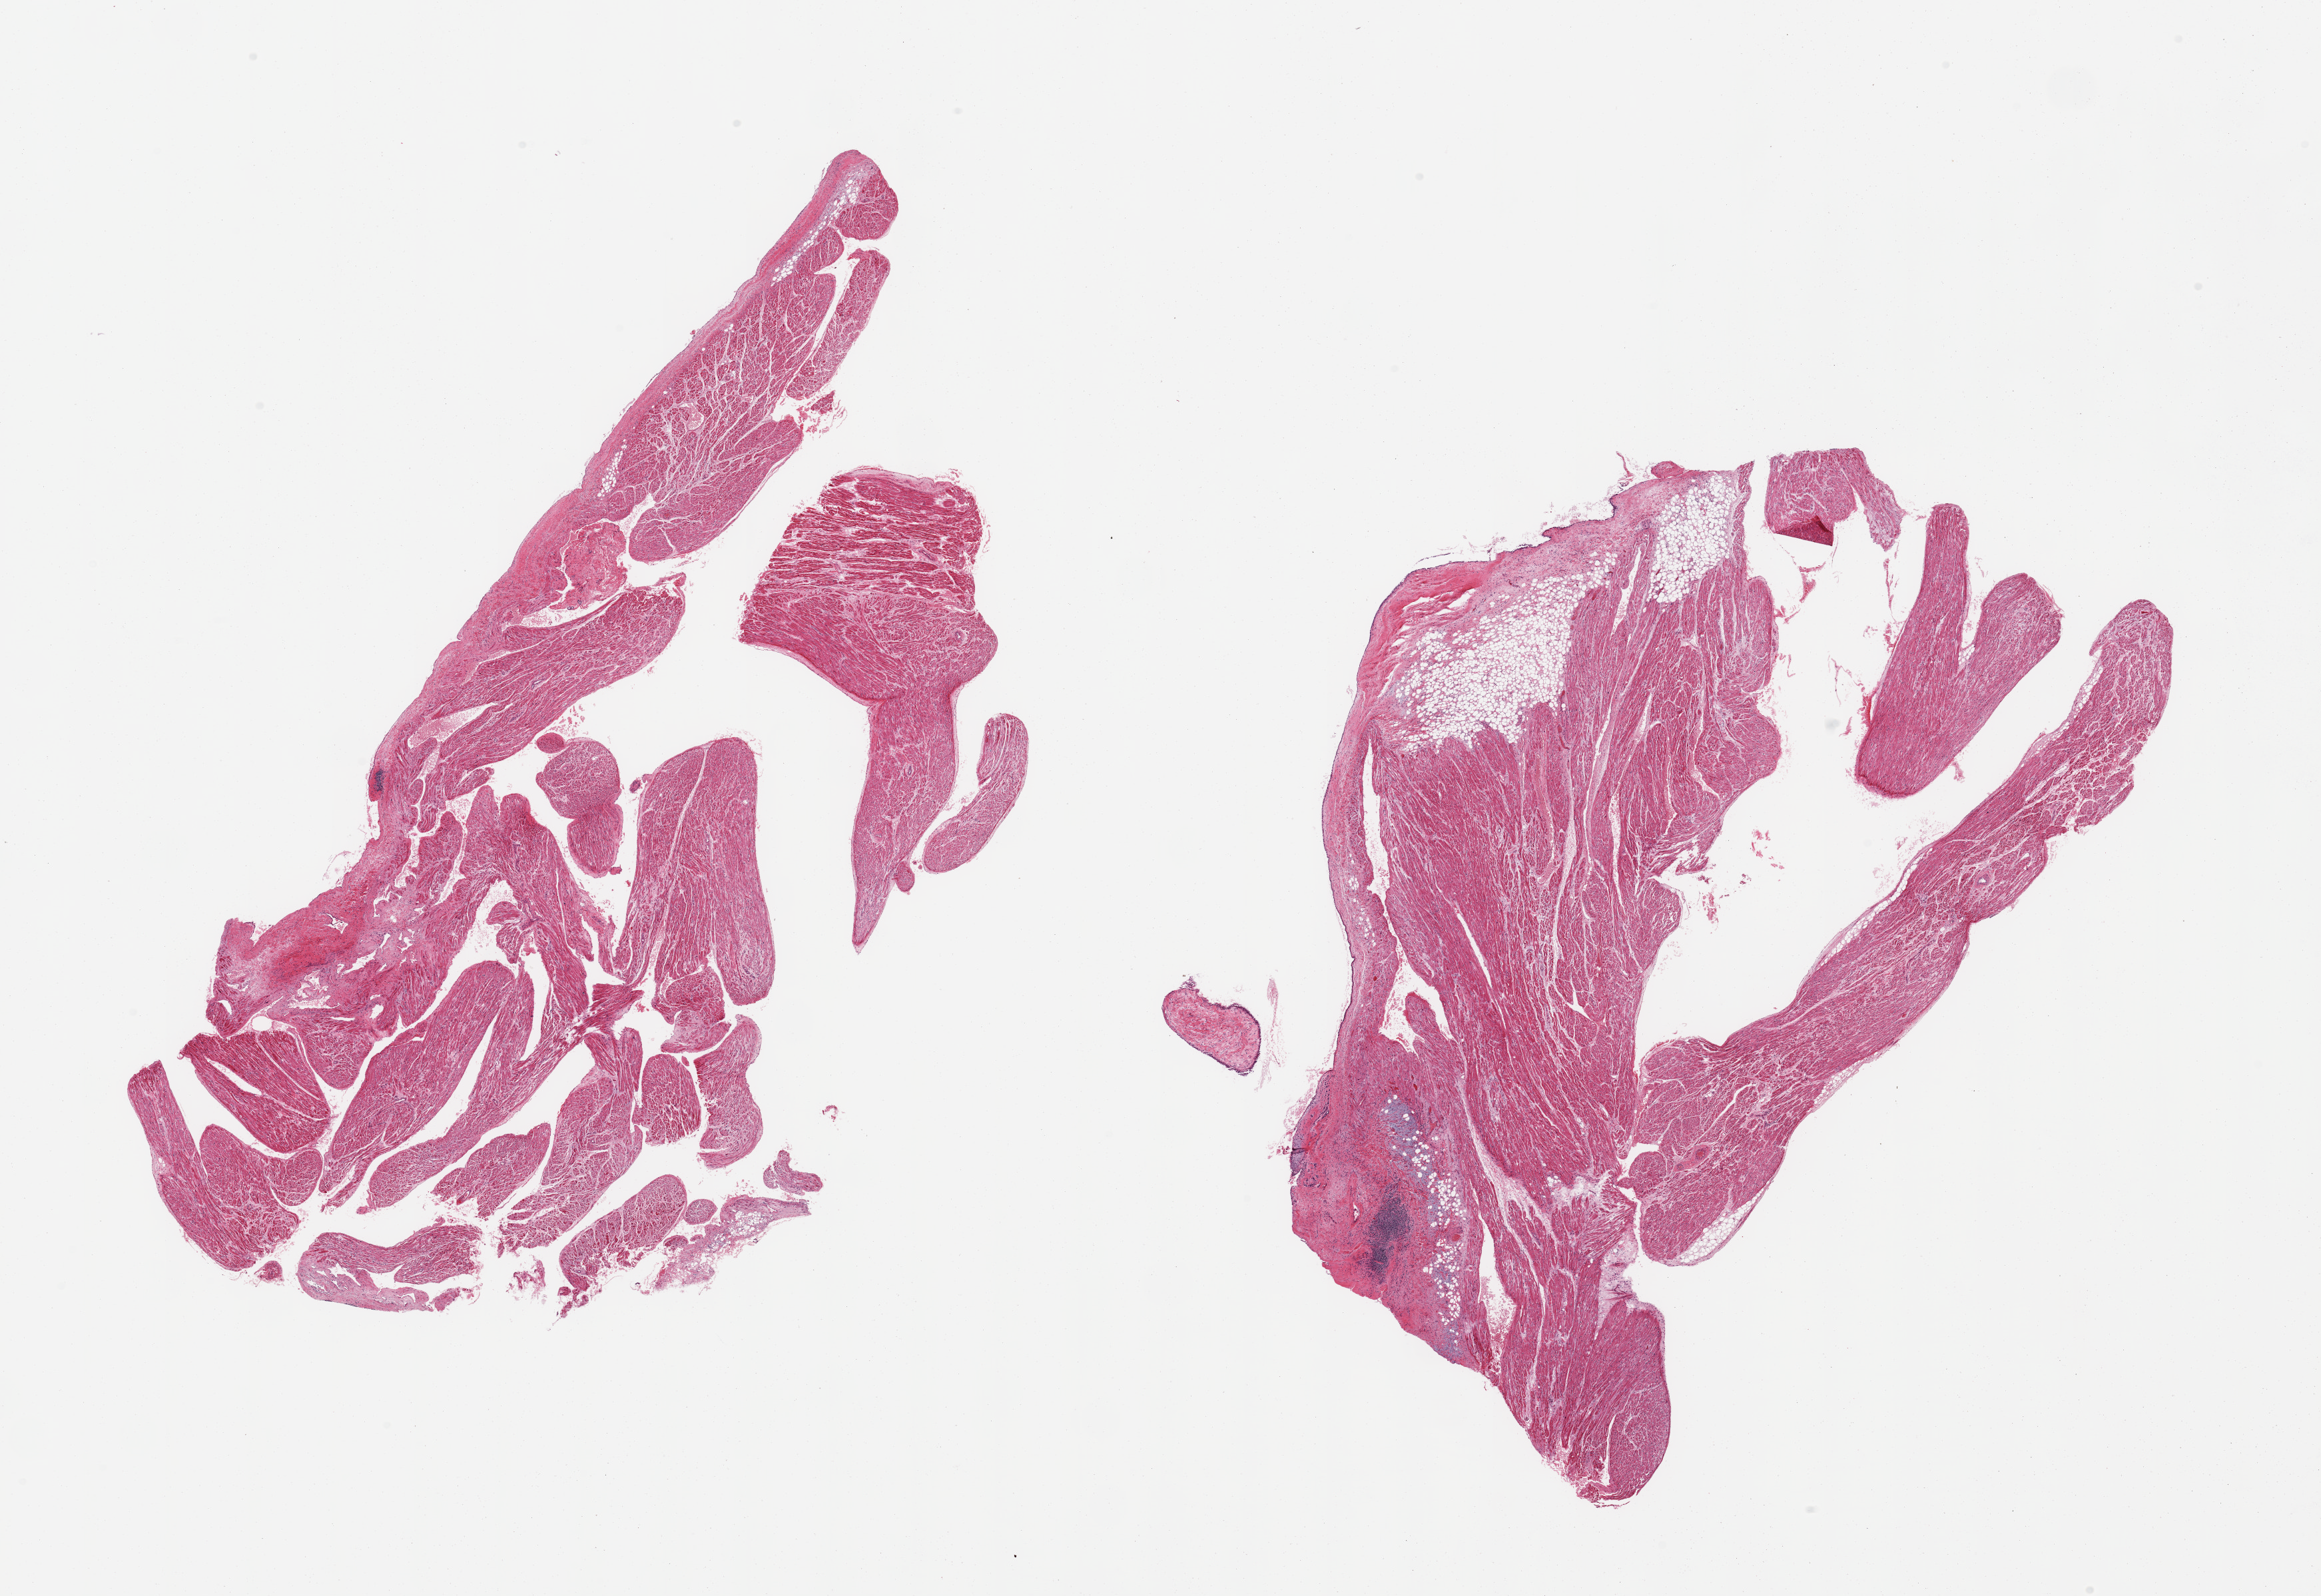
Digitized H&E-stained section, brightfield — shown as a low-resolution overview of the whole scanned area (about 27.6 x 19.0 mm, from a 20x scan). PAXgene-fixed paraffin-embedded (PFPE) section. Sampled site (target tissue): auricular appendage. Tissue donor sample. Male donor.
Pathologist's review note for this sample: 2 pieces; 20% fibrofatty tissue in 1 piece.